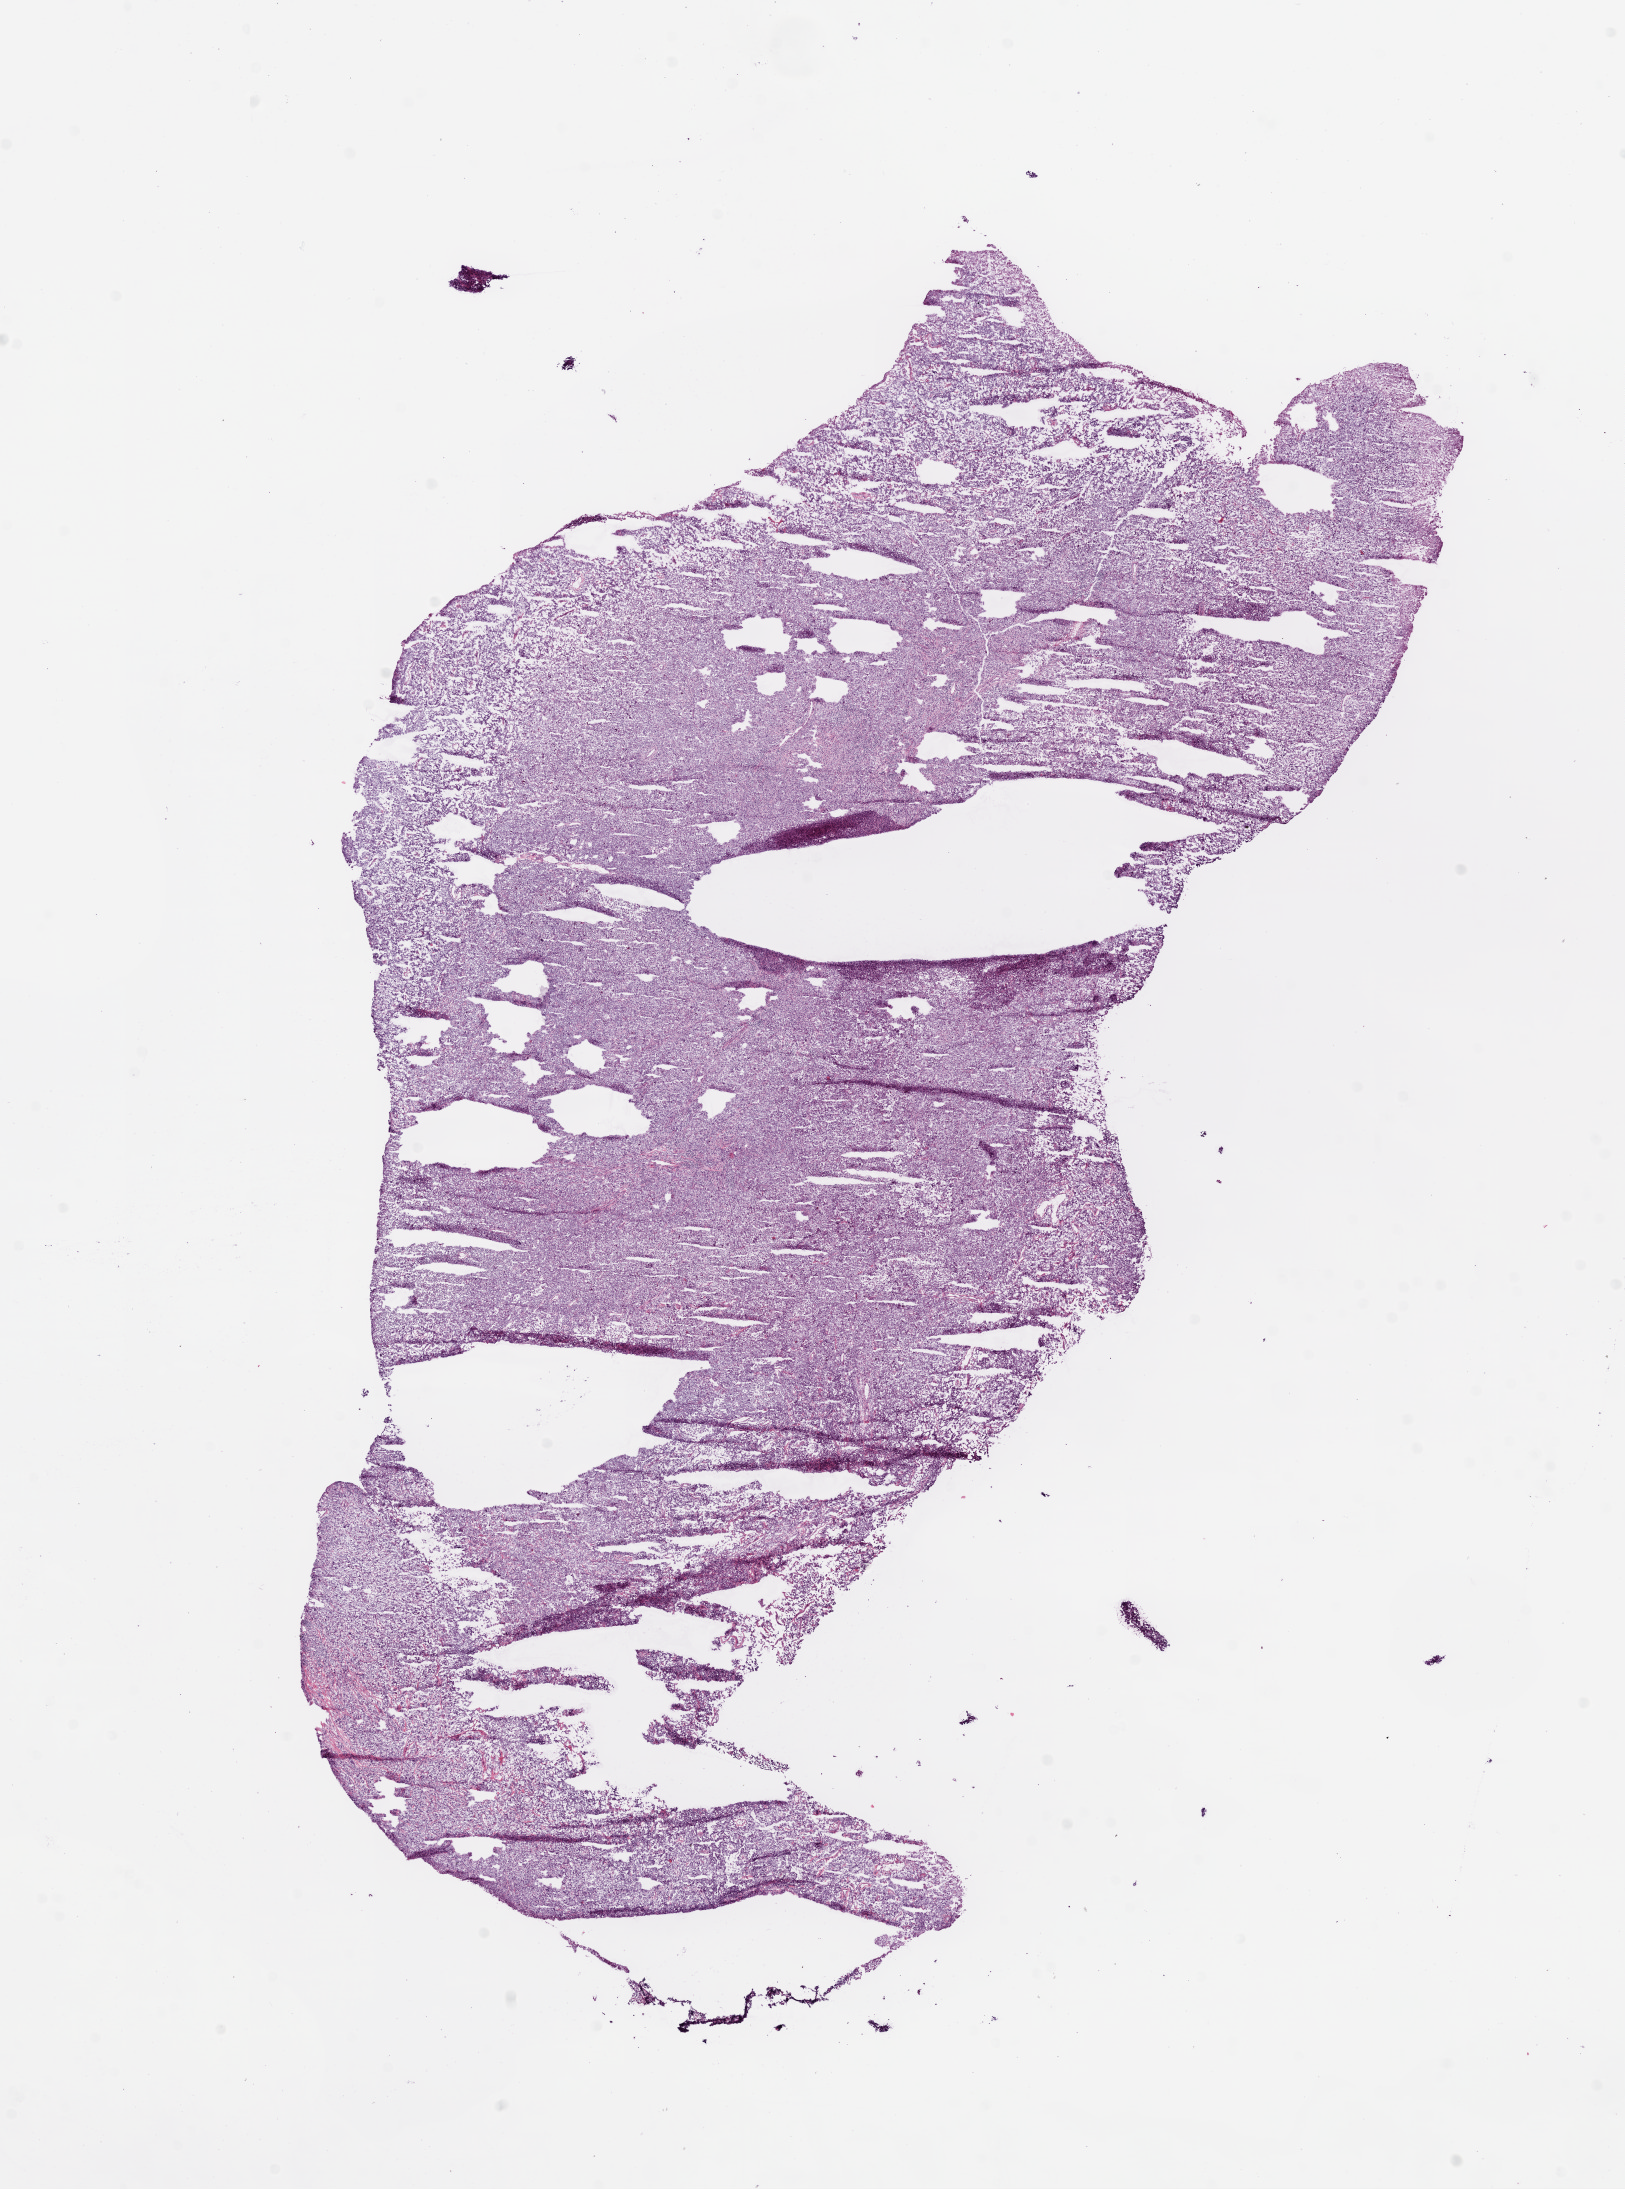
Hematoxylin and eosin (H&E) stained whole-slide image — a low-resolution overview of the entire scanned area, about 13.0 x 17.6 mm (slide scanned at 20x), frozen section, primary tumour sample from the lung. Male, age 69 years at initial diagnosis. Composition of this section per pathologist review: tumour cells 79%, tumour nuclei 80%.
Pathologic diagnosis: Squamous cell carcinoma, NOS (upper lobe, lung).